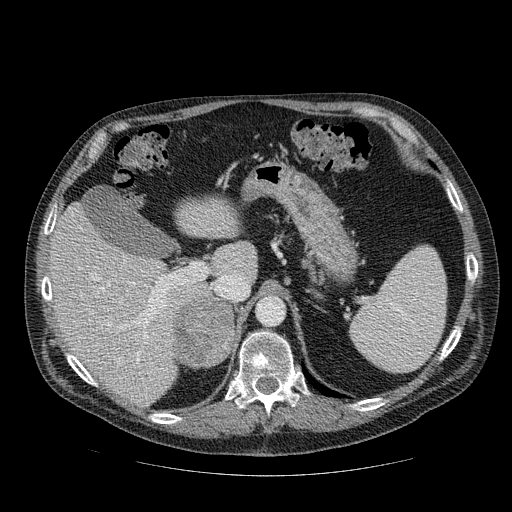
Contrast-enhanced abdominal CT, one axial slice; slice 65 of 111 in the series (ordered by position); reconstruction kernel STANDARD; intravenous contrast given; soft-tissue window (W 400 / L 40 HU); 512 × 512 image matrix. Patient: male, 56 years. Case-level facts recorded for this patient, not image findings: diagnosis: adrenocortical carcinoma; tumour side: right adrenal; tumour size at pathology: 9 cm; Ki-67 index: 48 %; stage (as recorded): 4.
Outlined on this slice (semi-automatic segmentation, software-assisted and operator-edited):
- mass: bounding box [x1, y1, x2, y2] px = [173, 295, 234, 365]